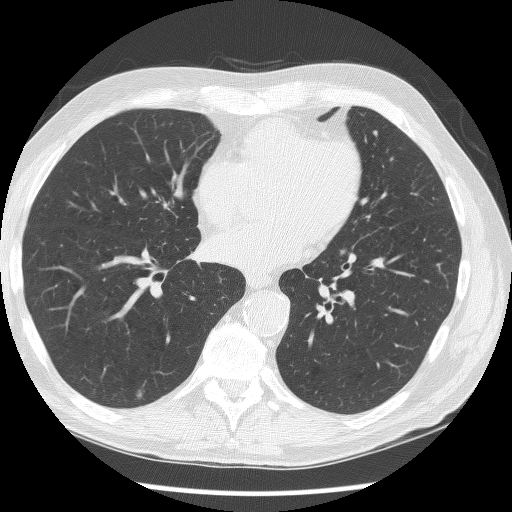
Low-dose screening chest CT, axial slice; baseline screening round; lung window (W 1500 / L -600 HU); 2.5 mm slice thickness; slice 103 of 190 in the series; 512 × 512 image matrix, field of view 340 × 340 mm. Male participant, aged 62 years at enrolment. Current smoker at enrolment.
Expert reader's lesion annotation, bounding box <122,382,162,410> (left, top, right, bottom; pixels). The screening reader recorded 2 non-calcified nodules or masses ≥4 mm on this exam (right lower lobe, right lower lobe); which of them this box marks is not recorded. Lung cancer was diagnosed 849 days after this screen: adenocarcinoma, NOS, right lower lobe, moderately differentiated (G2), stage IIIB (AJCC 6th edition), 15 mm at pathology.